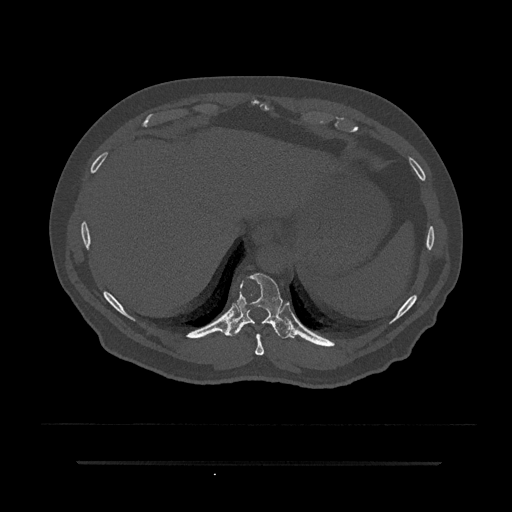
CT including the spine, one axial slice. Slice 341 of 797 in the series (ordered by position). Reconstruction kernel Br40s/3. Bone window (W 1800 / L 400 HU). 512 × 512 image matrix. Male patient, age 59 years. From the clinical record (not read from this slice): primary cancer: bile ducts; vertebrae with lytic lesions (as recorded): T10.
Structures marked on this image (semi-automatic segmentation, software-assisted and operator-edited):
- T10 vertebra: bounding box [x1, y1, x2, y2] px = [225, 273, 294, 339]
- T9 vertebra: [255, 333, 264, 356]